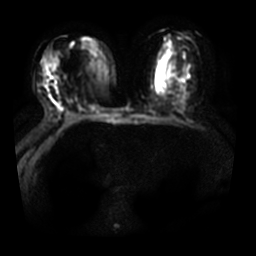
Breast MRI, one axial slice. Position 15 of 31 along the scan axis. Diffusion-weighted series; image 2 of 4 stored at this slice position (different b-values; order by instance number). 3 T. 5 mm slice thickness. 256 × 256 image matrix, field of view 350 × 350 mm. Female patient.
Structures marked on this image (expert manual segmentation):
- tumour on diffusion-weighted imaging: box from (x=44, y=59) to (x=54, y=79) px